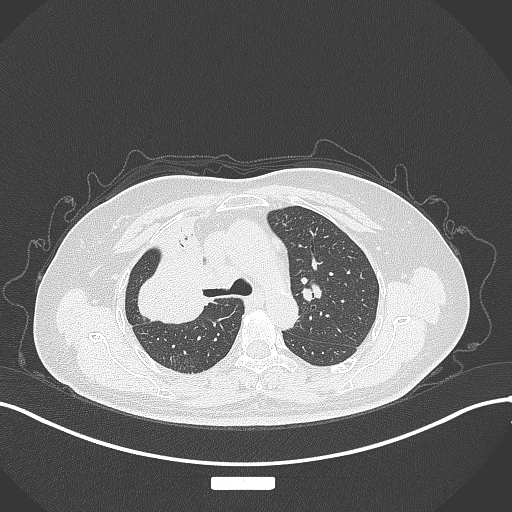
Chest CT, one axial slice. Slice 217 of 309 in the series (ordered by position). 120 kVp. Lung window (W 1500 / L -600 HU). 1 mm slice thickness. 512 × 512 image matrix. Female patient, age 60 years. From the clinical record (not read from this slice): clinical TNM (as recorded): T3 N1 M1.
Annotated regions visible in this slice (rectangle marked by the reading radiologist):
- lung tumour (recorded histology: adenocarcinoma): bounding box <136,243,222,329> (left, top, right, bottom; pixels)